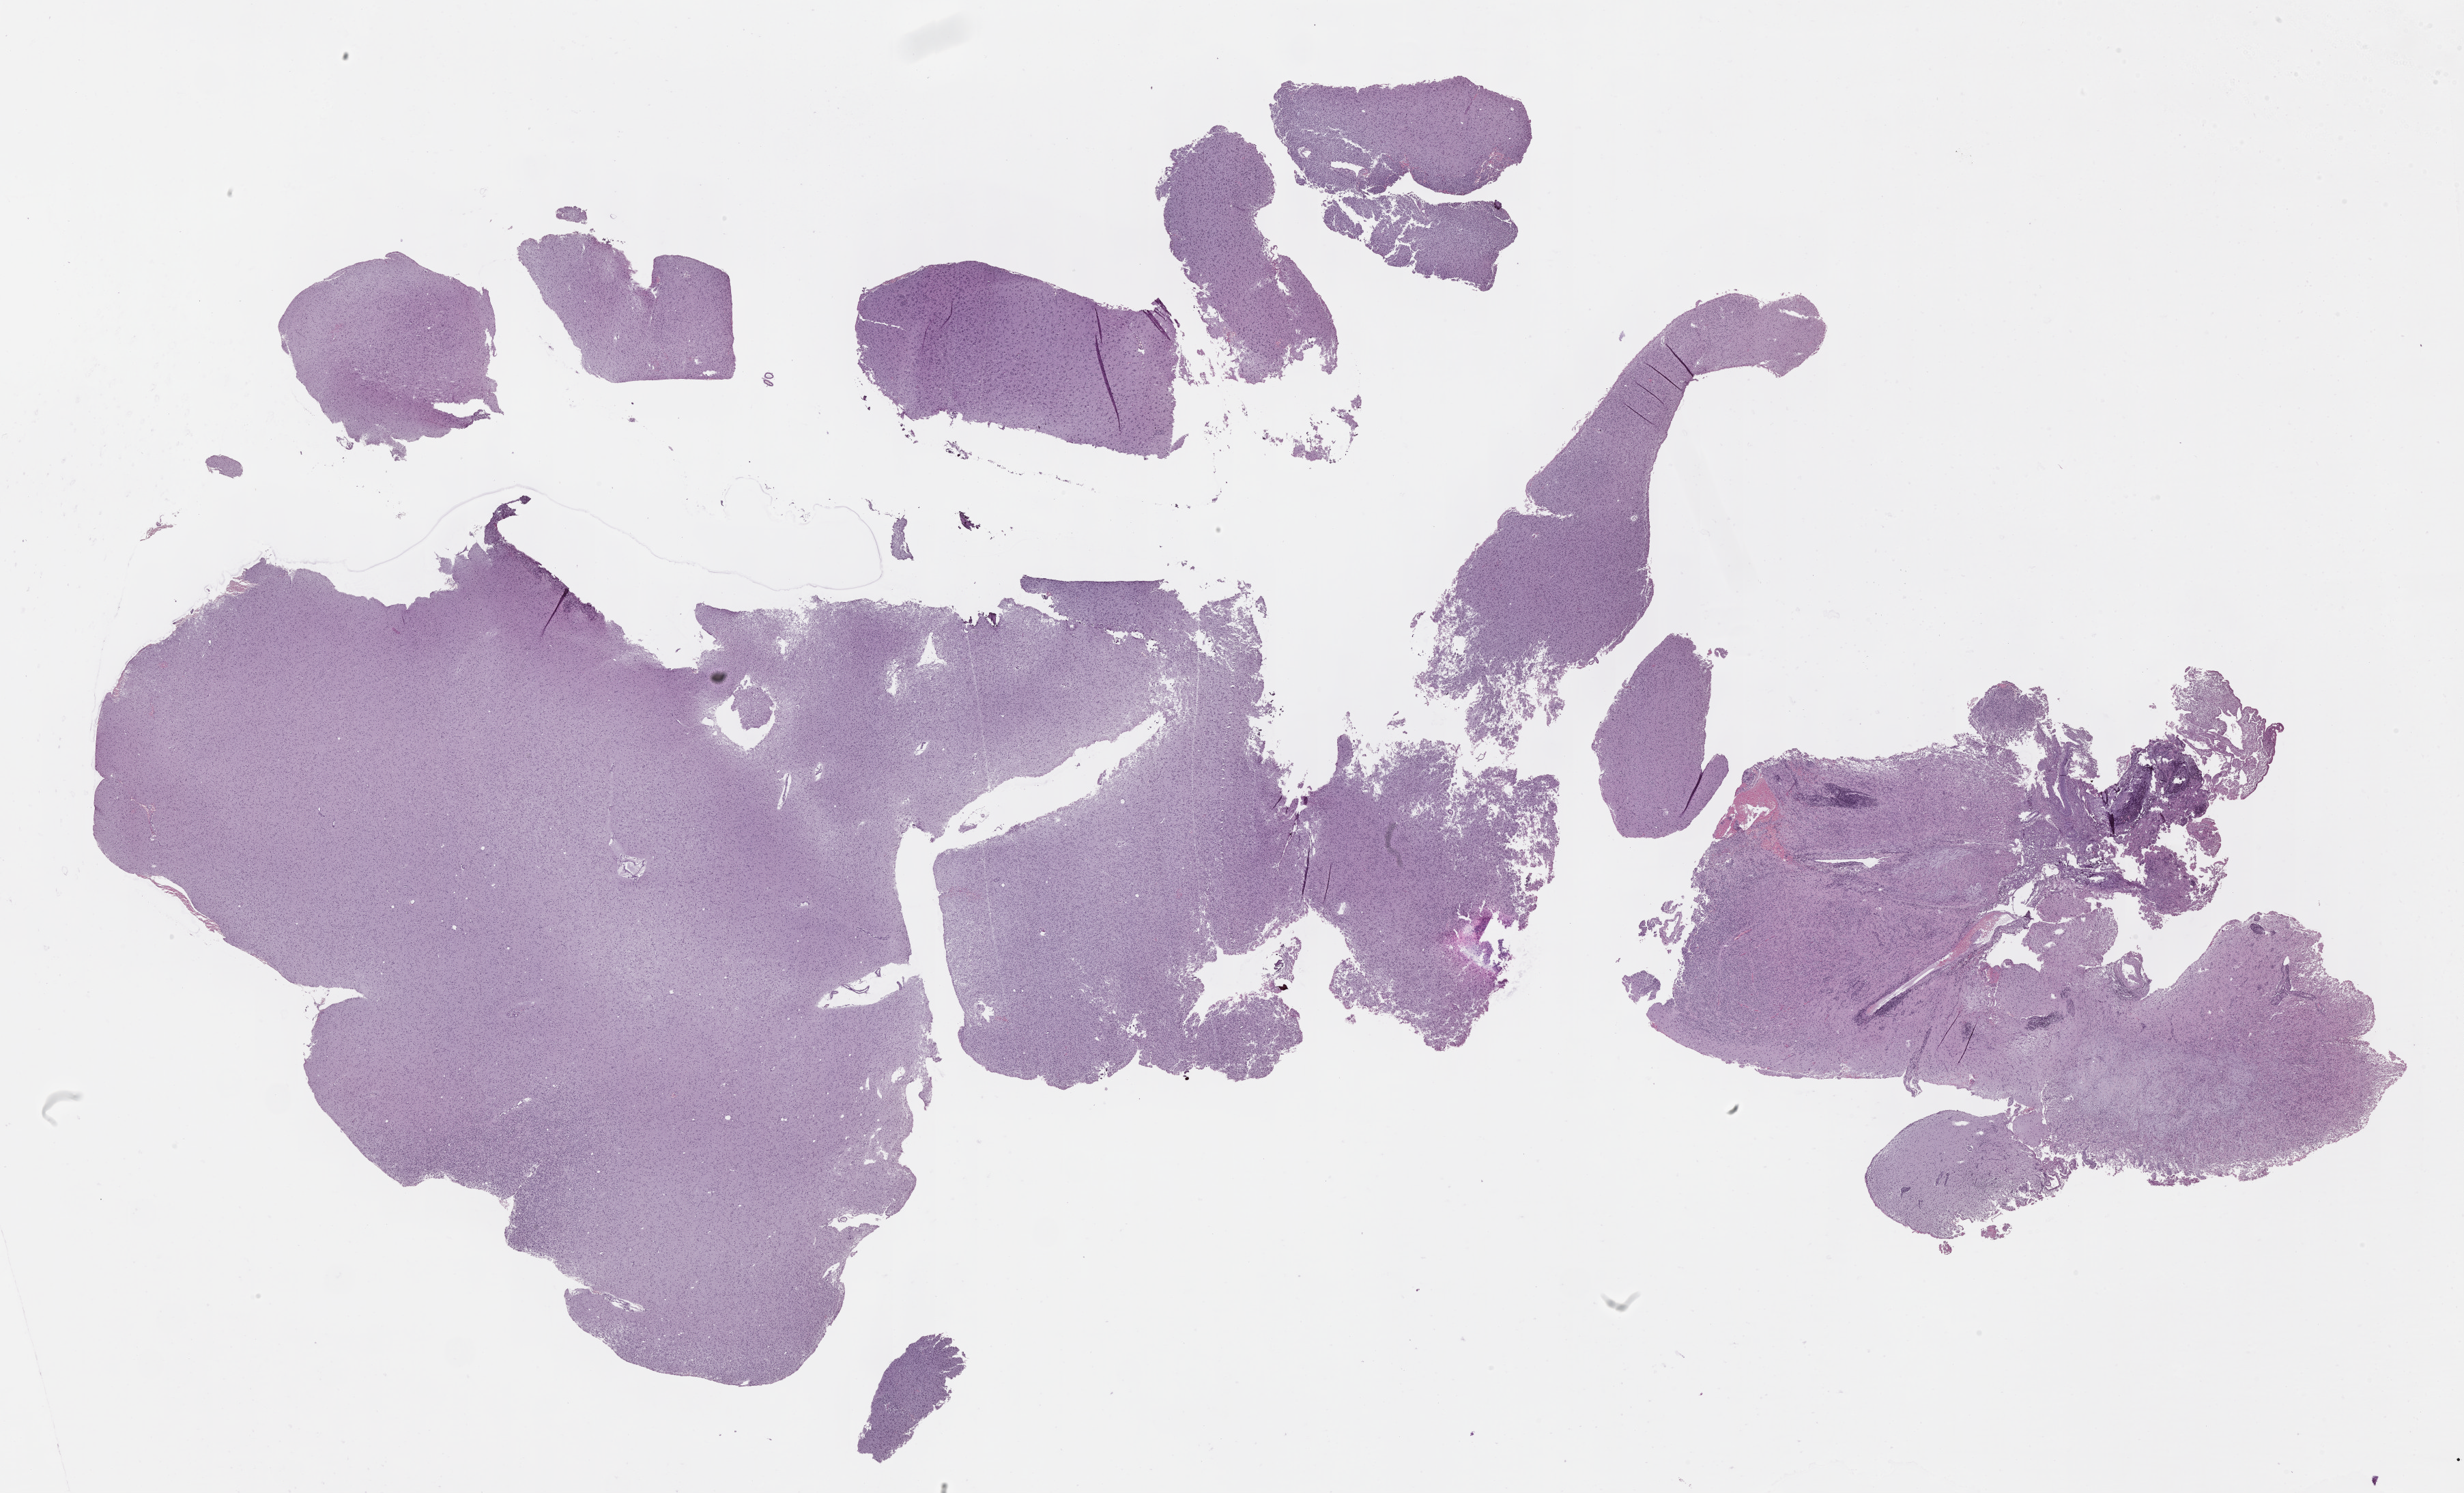
Digitized H&E tissue section (whole slide) — a low-resolution overview of the entire scanned area, about 29.2 x 17.7 mm (slide scanned at 40x). Formalin-fixed paraffin-embedded (FFPE) diagnostic section. Brain, primary tumour sample. Female patient; age at initial diagnosis 55 years.
Pathologic diagnosis: Mixed glioma (cerebrum).